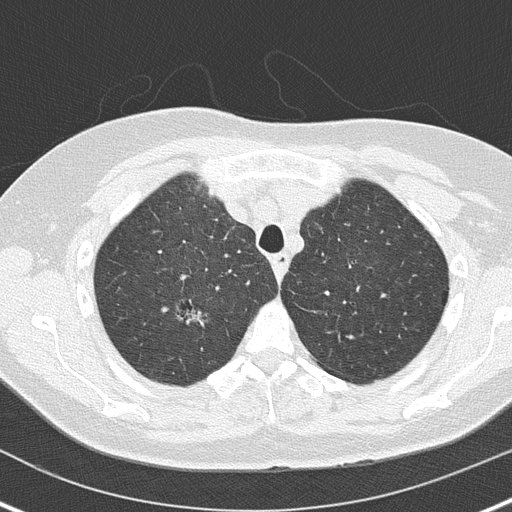
Low-dose screening chest CT, axial slice. Baseline annual screen. Lung window (W 1500 / L -600 HU). 120 kVp. 512 × 512 image matrix. Female participant, aged 61 years at enrolment.
Expert reader's lesion annotation, box from (x=181, y=300) to (x=218, y=332) px. Screening reader's record for this exam (one nodule recorded; not confirmed to be the boxed lesion): non-calcified nodule or mass ≥4 mm, right upper lobe, 8 × 5 mm, smooth margins, soft tissue attenuation. Official screen result: positive, change unspecified: nodule(s) >= 4 mm or enlarging nodule(s), mass(es), or other non-specific abnormalities suspicious for lung cancer. Participant outcome: lung cancer diagnosed 438 days after this screen — adenocarcinoma, NOS, right upper lobe, moderately differentiated (G2), stage IA (AJCC 6th edition), 20 mm at pathology.